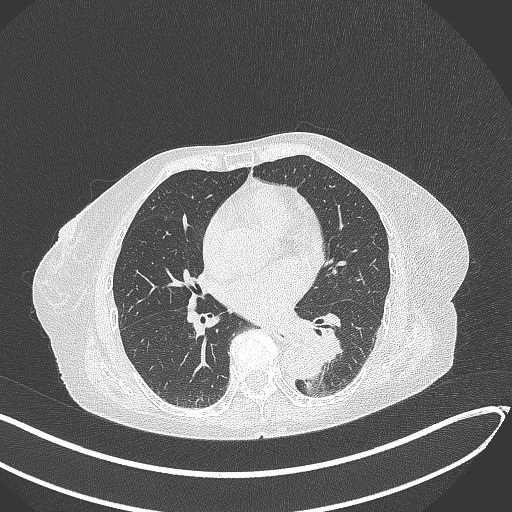
Chest CT, one axial slice; position 116 of 324 along the scan axis; reconstruction kernel B70f; 120 kVp; lung window (W 1500 / L -600 HU); 1 mm slice thickness; 512 × 512 image matrix, field of view 400 × 400 mm. Female patient, age 82 years. Case-level facts recorded for this patient, not image findings: clinical TNM (as recorded): T1b N0 M1.
Outlined on this slice (rectangle marked by the reading radiologist):
- lung tumour (recorded histology: adenocarcinoma): bounding box [x1, y1, x2, y2] px = [297, 321, 347, 366]